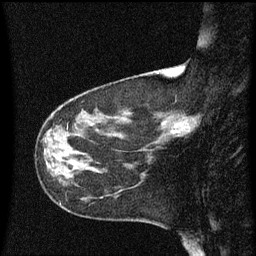
Breast MRI (dynamic contrast-enhanced), one sagittal slice. Position 21 of 60 along the scan axis. Dynamic contrast-enhanced series, image 2 of 3 at this slice position (ordered by acquisition). 1.5 T. TE 4.2 ms, TR 8.4 ms. 2 mm slice thickness. 256 × 256 image matrix, field of view 200 × 200 mm. Patient: female, 41 years. Case-level facts recorded for this patient, not image findings: setting: breast cancer imaged before/during neoadjuvant chemotherapy; receptor status: triple-negative.
Outlined on this slice (semi-automatic segmentation, software-assisted and operator-edited):
- analysis volume of interest (the breast-tissue region the enhancement analysis was run in; not a lesion): bounding box [x1, y1, x2, y2] px = [158, 100, 200, 145]
- tumour enhancement mask (voxels above the 70 % enhancement threshold inside the analysis volume of interest): [188, 118, 197, 133]